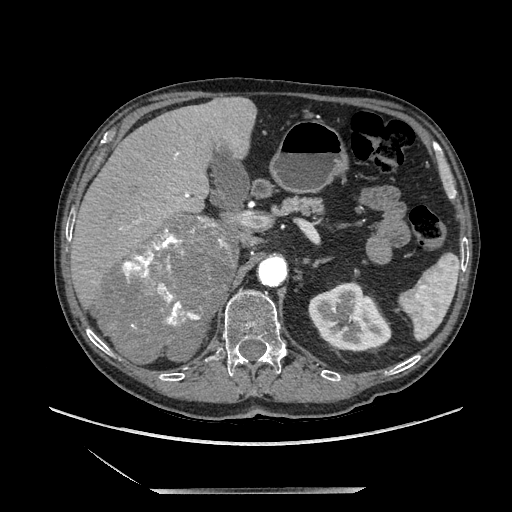
Contrast-enhanced abdominal CT, one axial slice. Position 128 of 243 along the scan axis. Soft-tissue window (W 400 / L 40 HU). 512 × 512 image matrix, field of view 420 × 420 mm. Male patient. From the clinical record (not read from this slice): diagnosis: adrenocortical carcinoma; tumour side: right adrenal; tumour size at pathology: 16 cm; Ki-67 index: 17 %; stage (as recorded): 3.
Outlined on this slice (semi-automatic segmentation, software-assisted and operator-edited):
- mass: box from (x=96, y=216) to (x=235, y=363) px